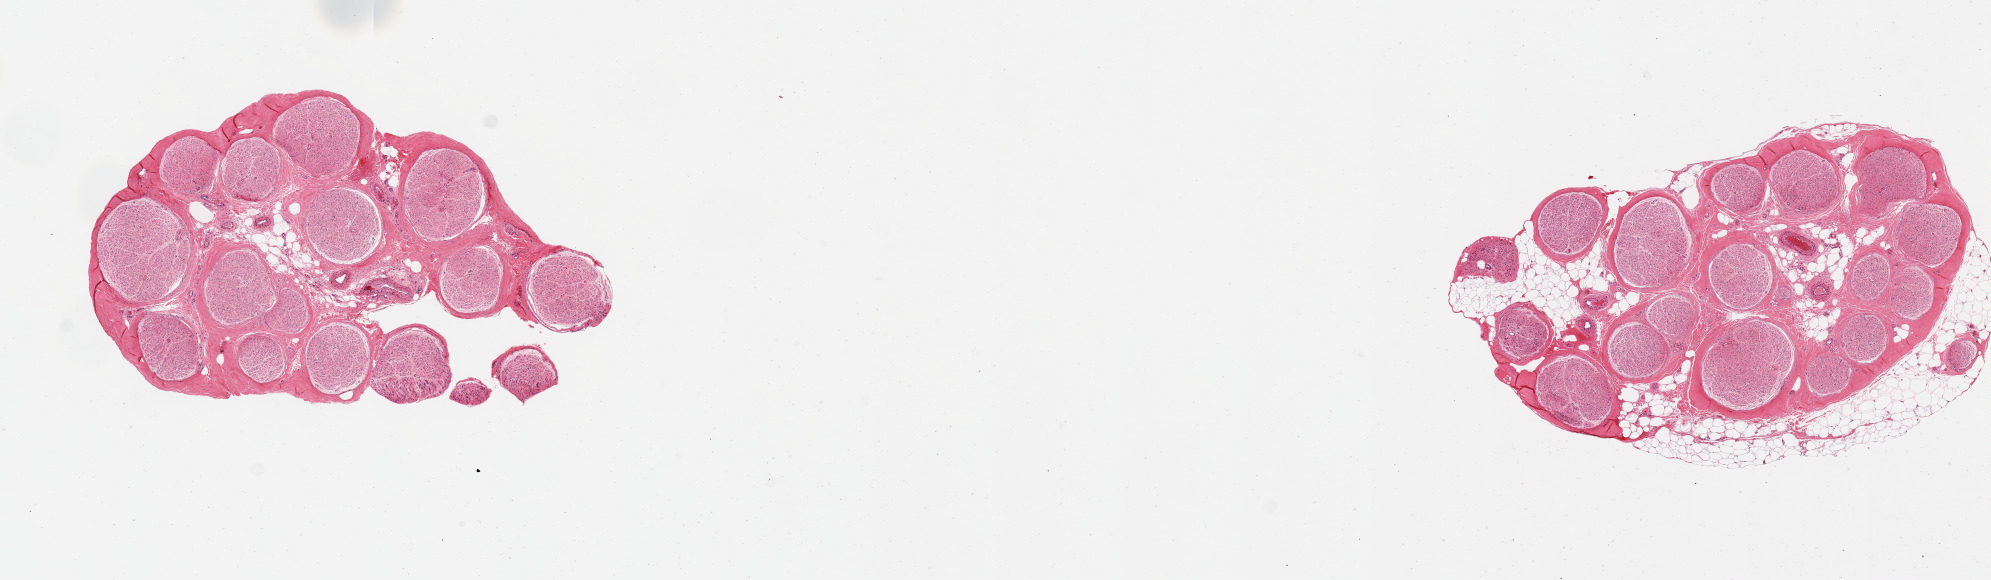
Whole-slide image, H&E stain — low-resolution overview of the scanned area, about 15.8 x 4.6 mm, PAXgene-fixed paraffin-embedded (PFPE) section, target tissue: tibial nerve, tissue donor sample. Donor: male.
* reviewer comment on this tissue sample: 2 pieces, generally clean; small ~0.5mm nubbin of adherent fat on one section